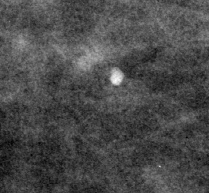
Region of interest cut from a scanned film mammogram (one marked finding), left breast, CC view, BI-RADS breast density category 2 (scale 1–4).
Finding: calcifications, morphology punctate; BI-RADS assessment category 2; benign without callback (not worked up further).